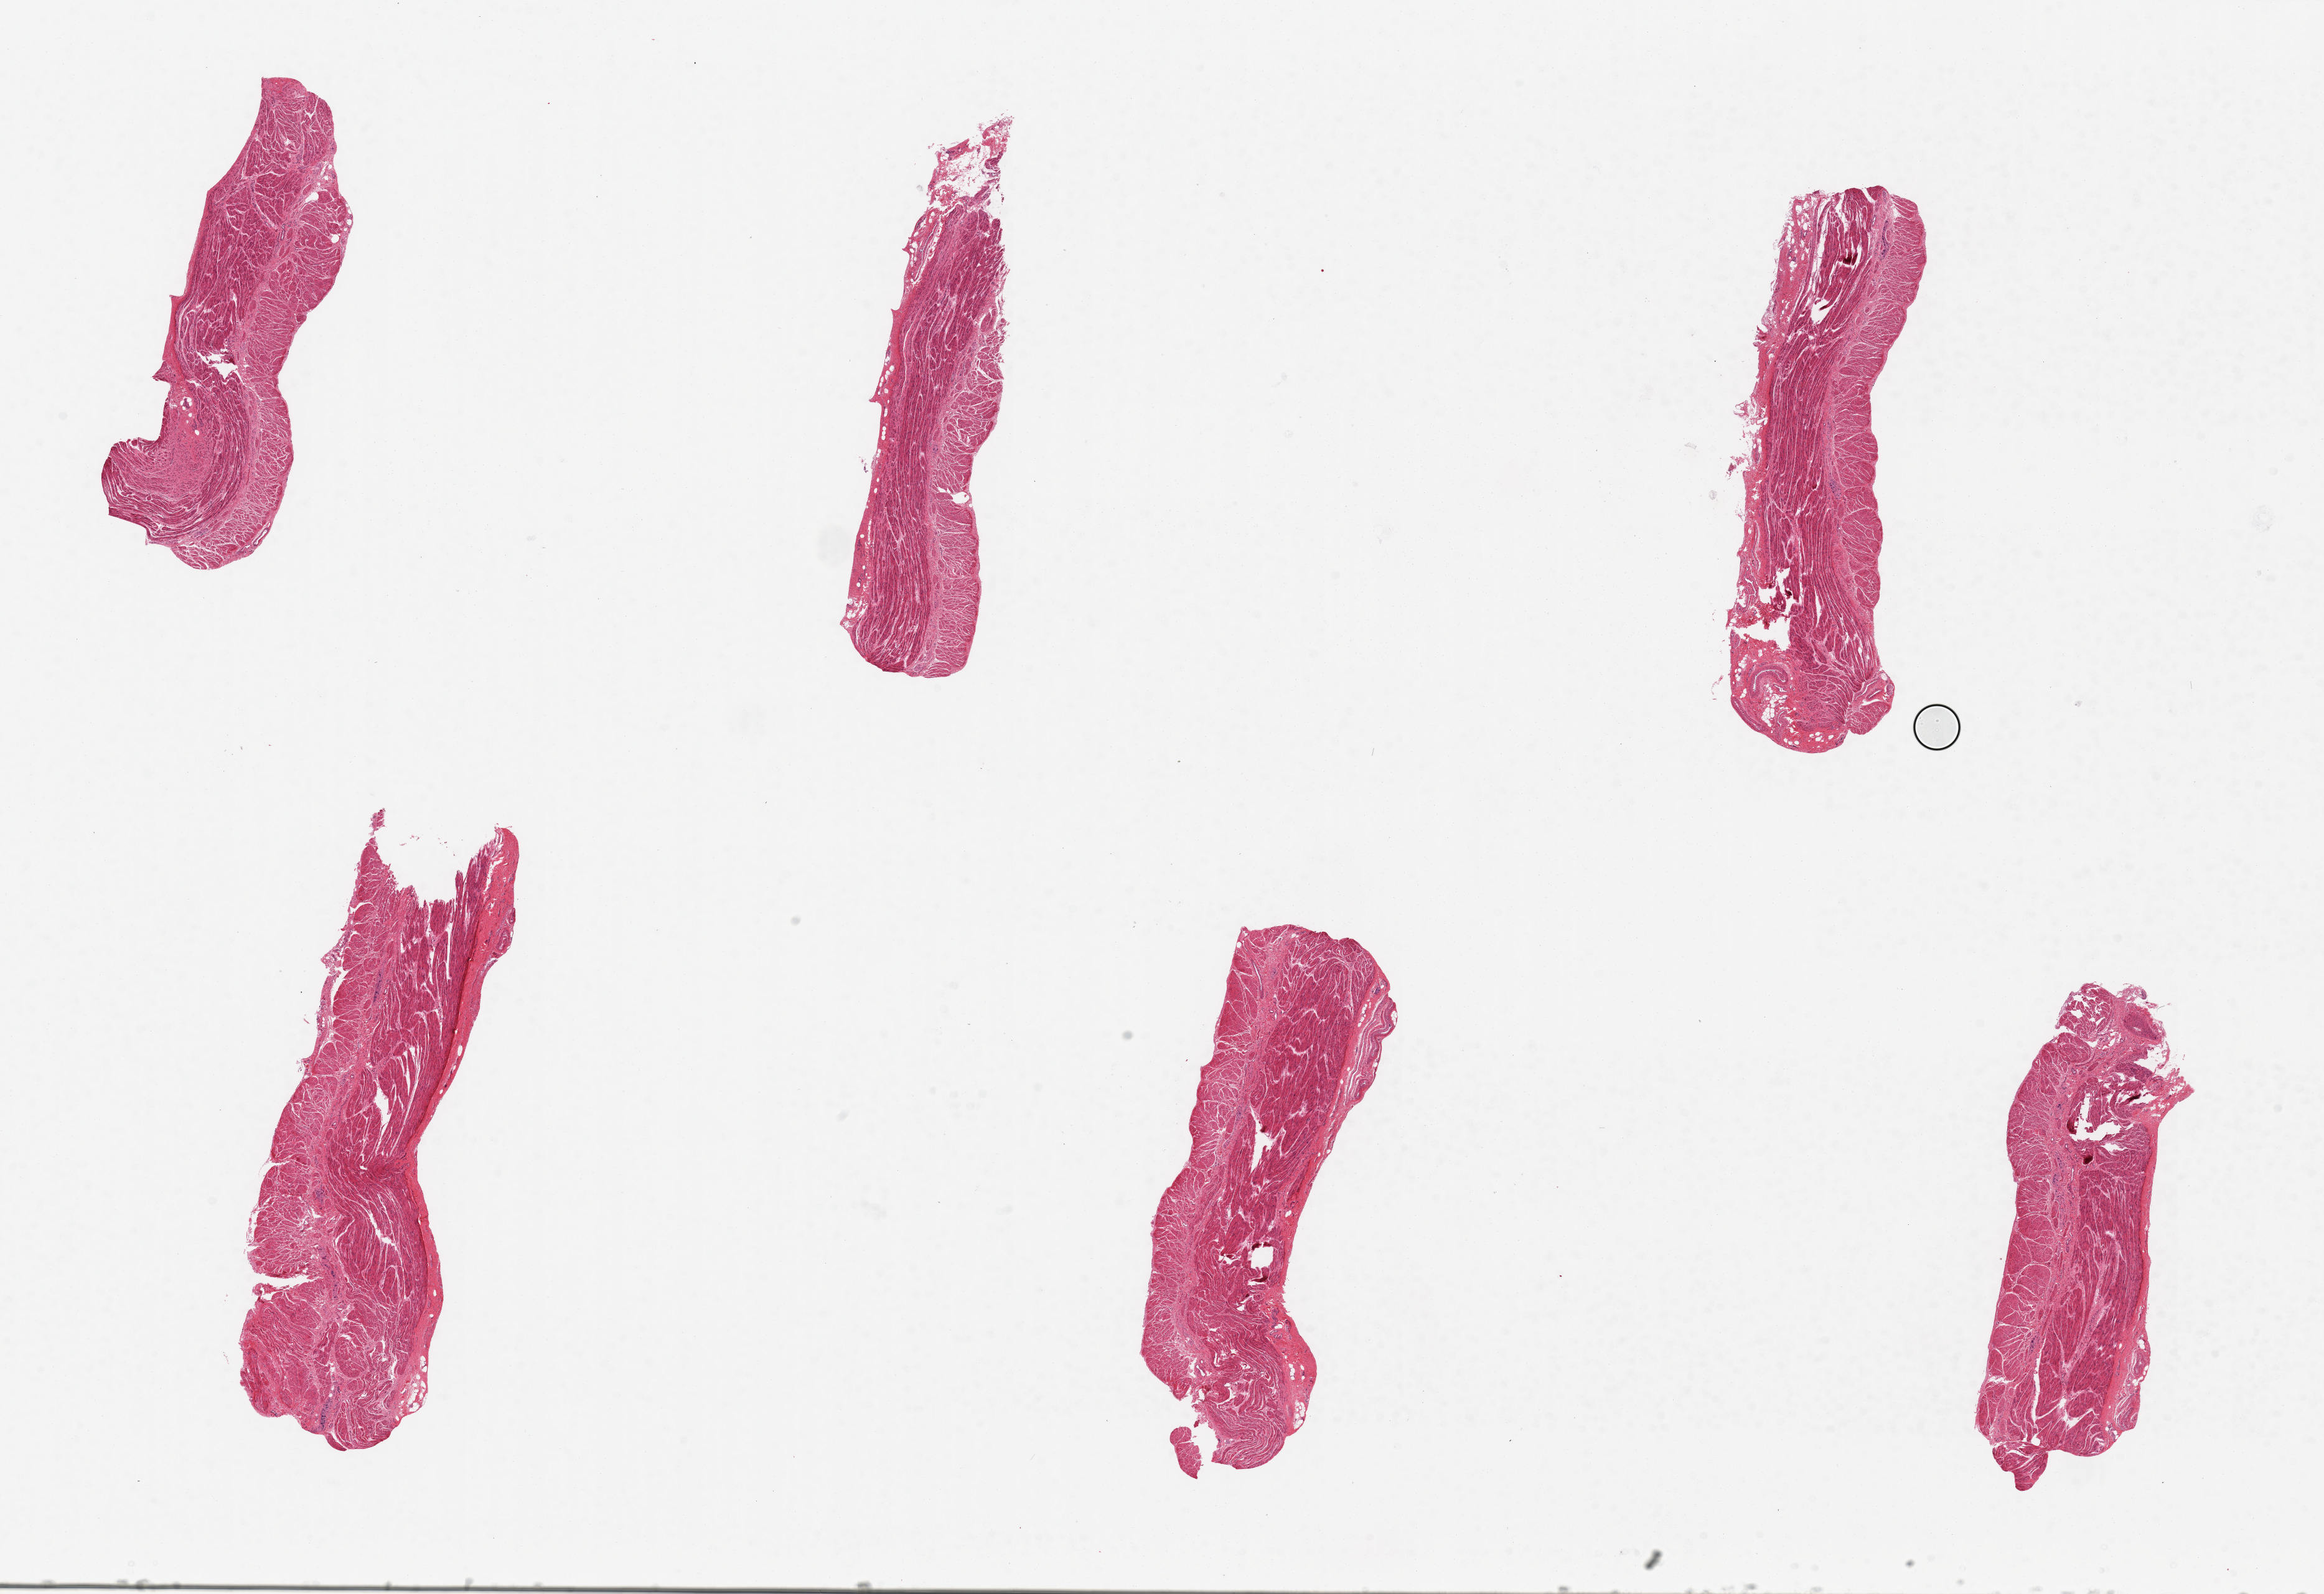
Whole-slide image, hematoxylin and eosin (H&E) stain, brightfield, a low-resolution overview of the entire scanned area, about 29.5 x 20.3 mm, PAXgene-fixed paraffin-embedded (PFPE) section, sampled site (target tissue): gastroesophageal junction, tissue donor sample.
Reviewer comment on this tissue sample: 6 pieces, up to 8x2mm; all with good muscularis and no adipose.